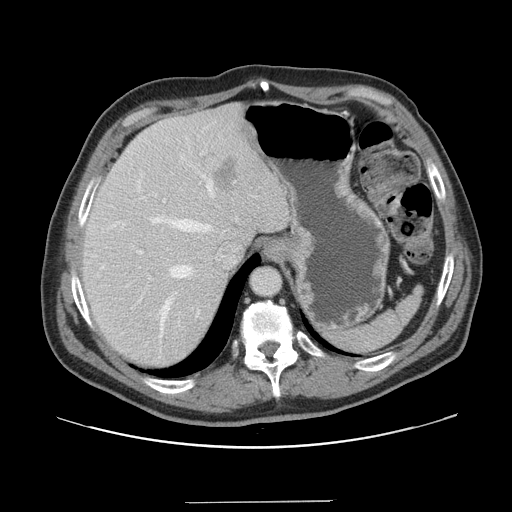
Contrast-enhanced abdominal CT, one axial slice; slice 120 of 151 in the series (ordered by position); intravenous contrast given; soft-tissue window (W 400 / L 40 HU); 2.5 mm slice thickness; 512 × 512 image matrix, field of view 399 × 399 mm. Male patient, age 63 years. From the clinical record (not read from this slice): diagnosis: colorectal cancer liver metastases, imaged before liver resection; multiple liver metastases: no; largest metastasis: 2.1 cm.
Annotated regions visible in this slice (manually delineated by an expert):
- hepatic veins: bounding box (x1, y1, x2, y2) in pixels: (138, 180, 214, 332)
- liver: (81, 106, 290, 368)
- planned liver remnant (the part of the liver to remain after resection): (81, 117, 256, 368)
- portal vein (with intrahepatic branches): (137, 153, 203, 279)
- liver metastasis: (209, 156, 236, 189)